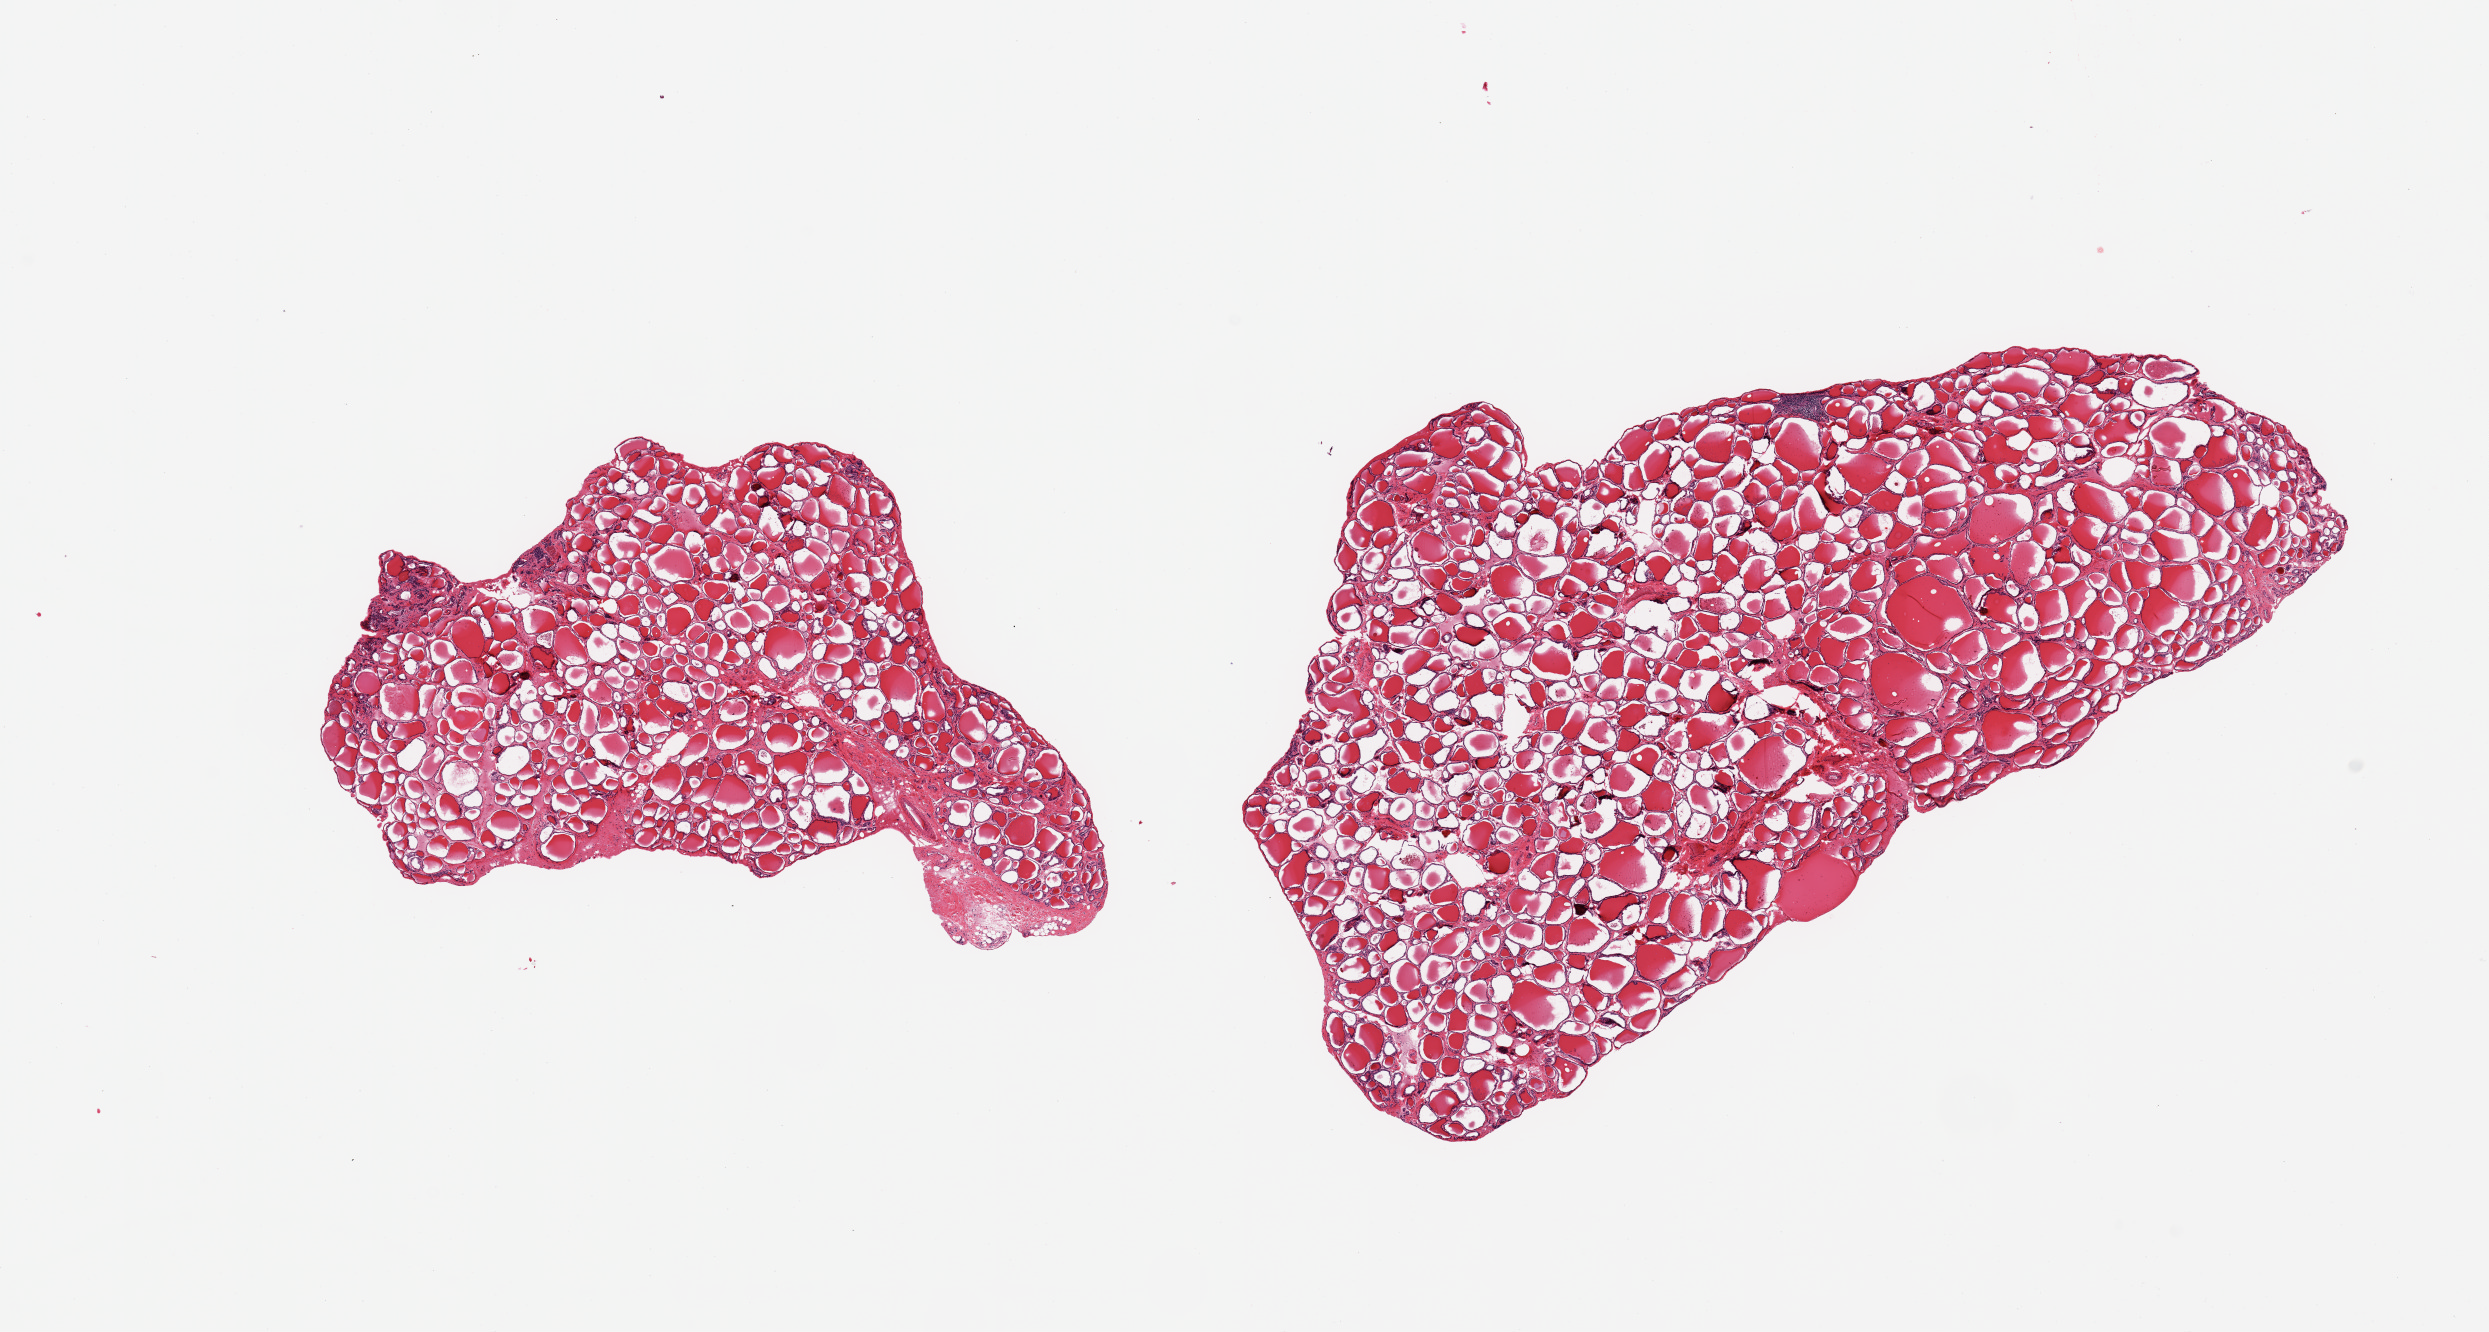
Hematoxylin and eosin (H&E) whole-slide image, brightfield, whole scanned area (about 19.7 x 10.5 mm, from a 20x scan) shown as a low-resolution overview. PAXgene-fixed paraffin-embedded (PFPE) section. Sampled site (target tissue): thyroid. Tissue donor sample. Donor sex: male.
Pathologist's review note for this sample: 2 pieces; no abnormalities.